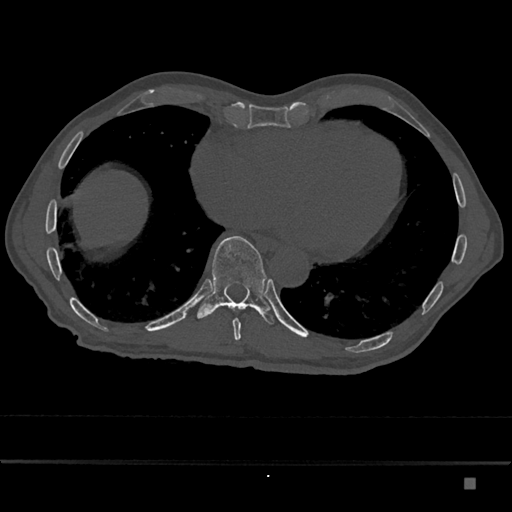
CT including the spine, one axial slice; slice 761 of 797 in the series (ordered by position); reconstruction kernel Br40s/3; 120 kVp; bone window (W 1800 / L 400 HU); 0.5 mm slice thickness; 512 × 512 image matrix, field of view 390 × 390 mm. Male patient, age 72 years. Case-level facts recorded for this patient, not image findings: primary cancer: prostate.
Annotated regions visible in this slice (semi-automatic segmentation, software-assisted and operator-edited):
- T10 vertebra: box from (x=197, y=236) to (x=275, y=325) px
- T9 vertebra: (x=233, y=309)–(x=244, y=340)